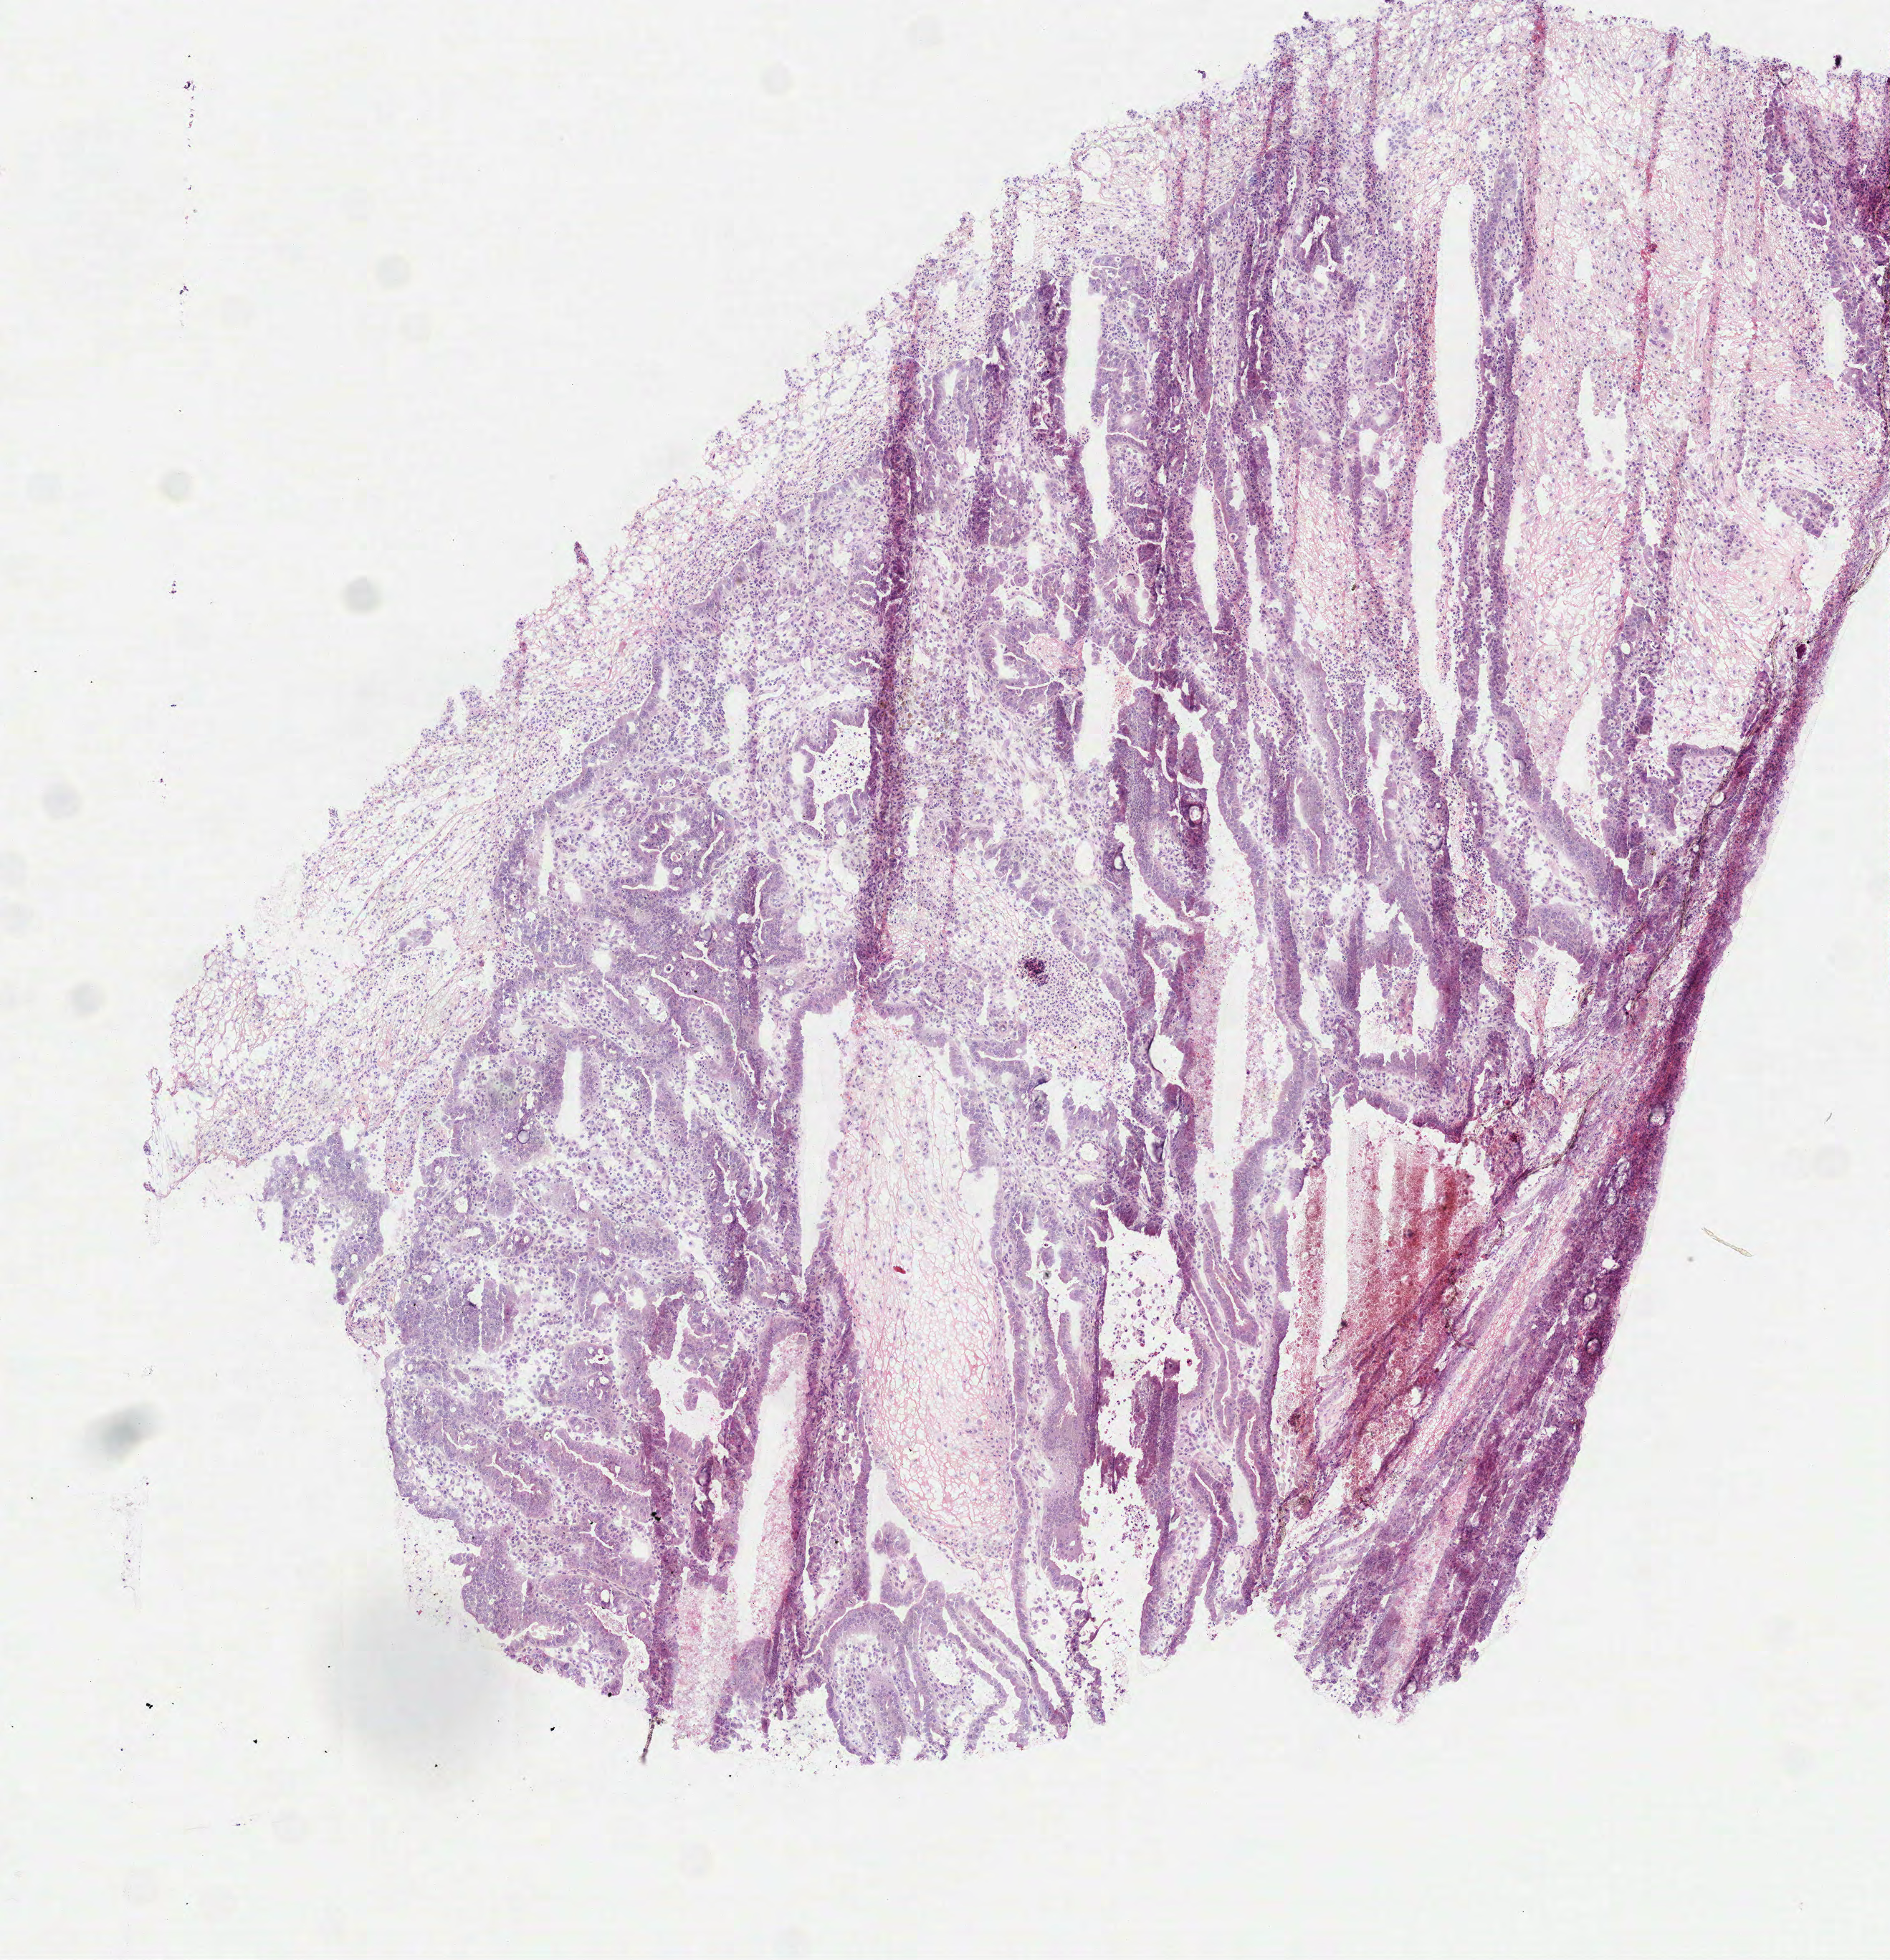
H&E-stained whole-slide image, shown as a low-resolution overview of the whole scanned area (about 5.3 x 5.5 mm); frozen section from the top of the tissue portion; sample: primary tumour, stomach. Male patient; age at initial diagnosis 64 years. Histologic grade: G2 (moderately differentiated). Slide review estimates, as recorded: tumour cells 77%, tumour nuclei 75%, normal cells 0%, stromal cells 15%, necrosis 8%.
• histologic diagnosis: Tubular adenocarcinoma (body of stomach)
• lymph nodes positive (case pathology): 5 of 14 examined
• AJCC pathologic stage: IIB